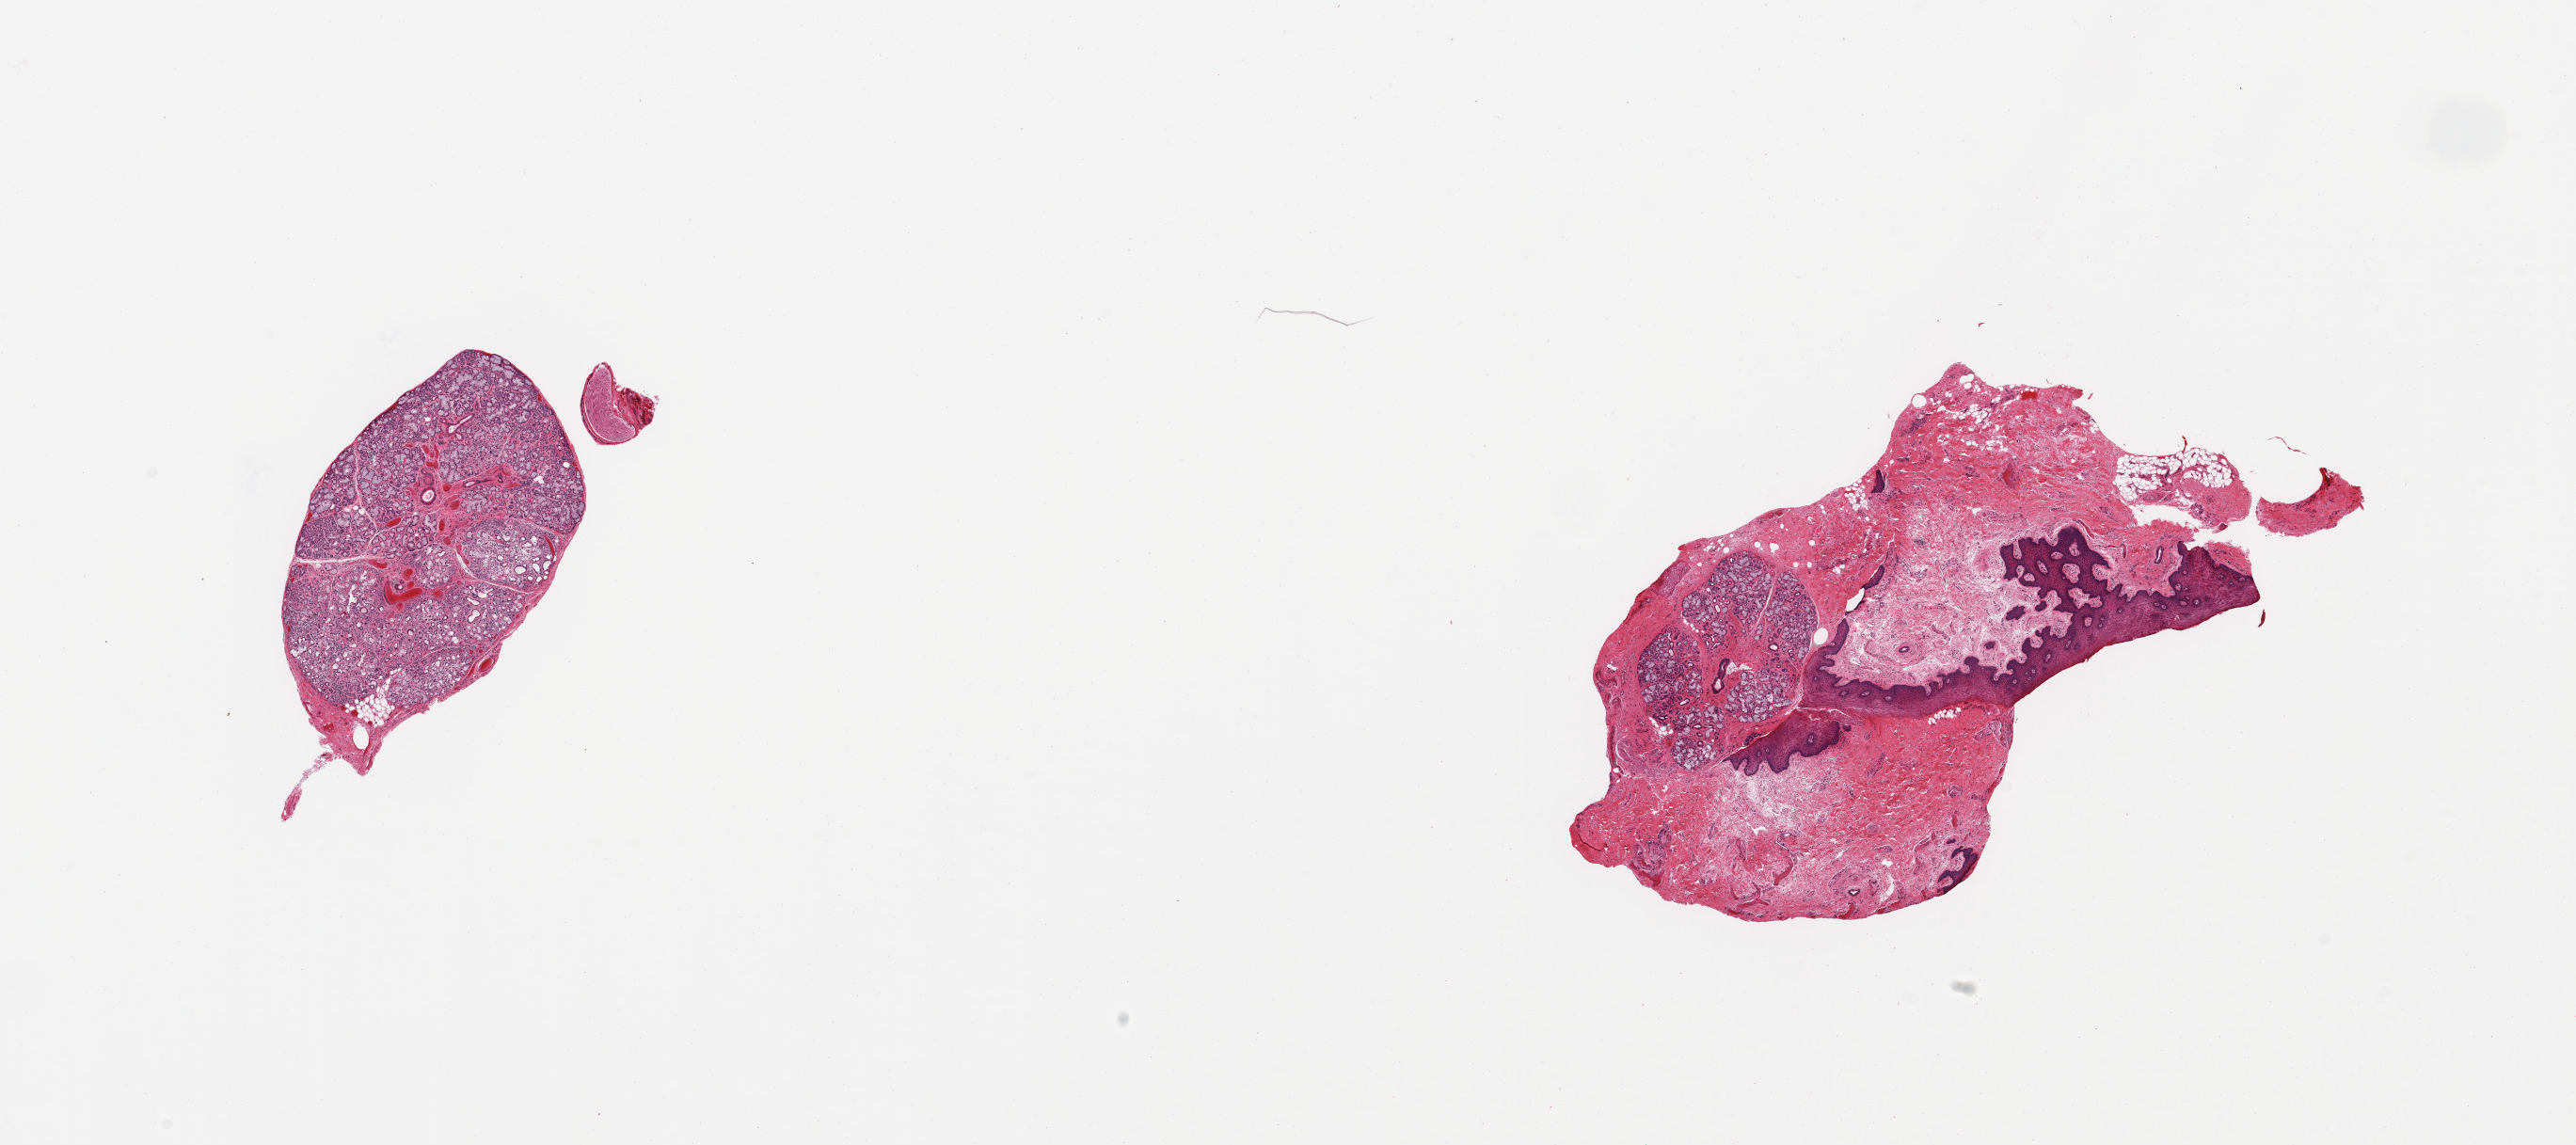
H&E whole-slide image, shown as a low-resolution overview of the whole scanned area (about 21.7 x 9.6 mm, slide scanned at 20x); PAXgene-fixed, paraffin-embedded tissue; sampled site (target tissue): minor salivary gland; donor tissue sample. Donor: male.
Review note (as recorded): 2 pieces; 1 piece is salivary gland elements with mild chronic inflammation and detached nerve fragment, 2nd is ~10-15% salivary gland surrounded by lip/stroma.